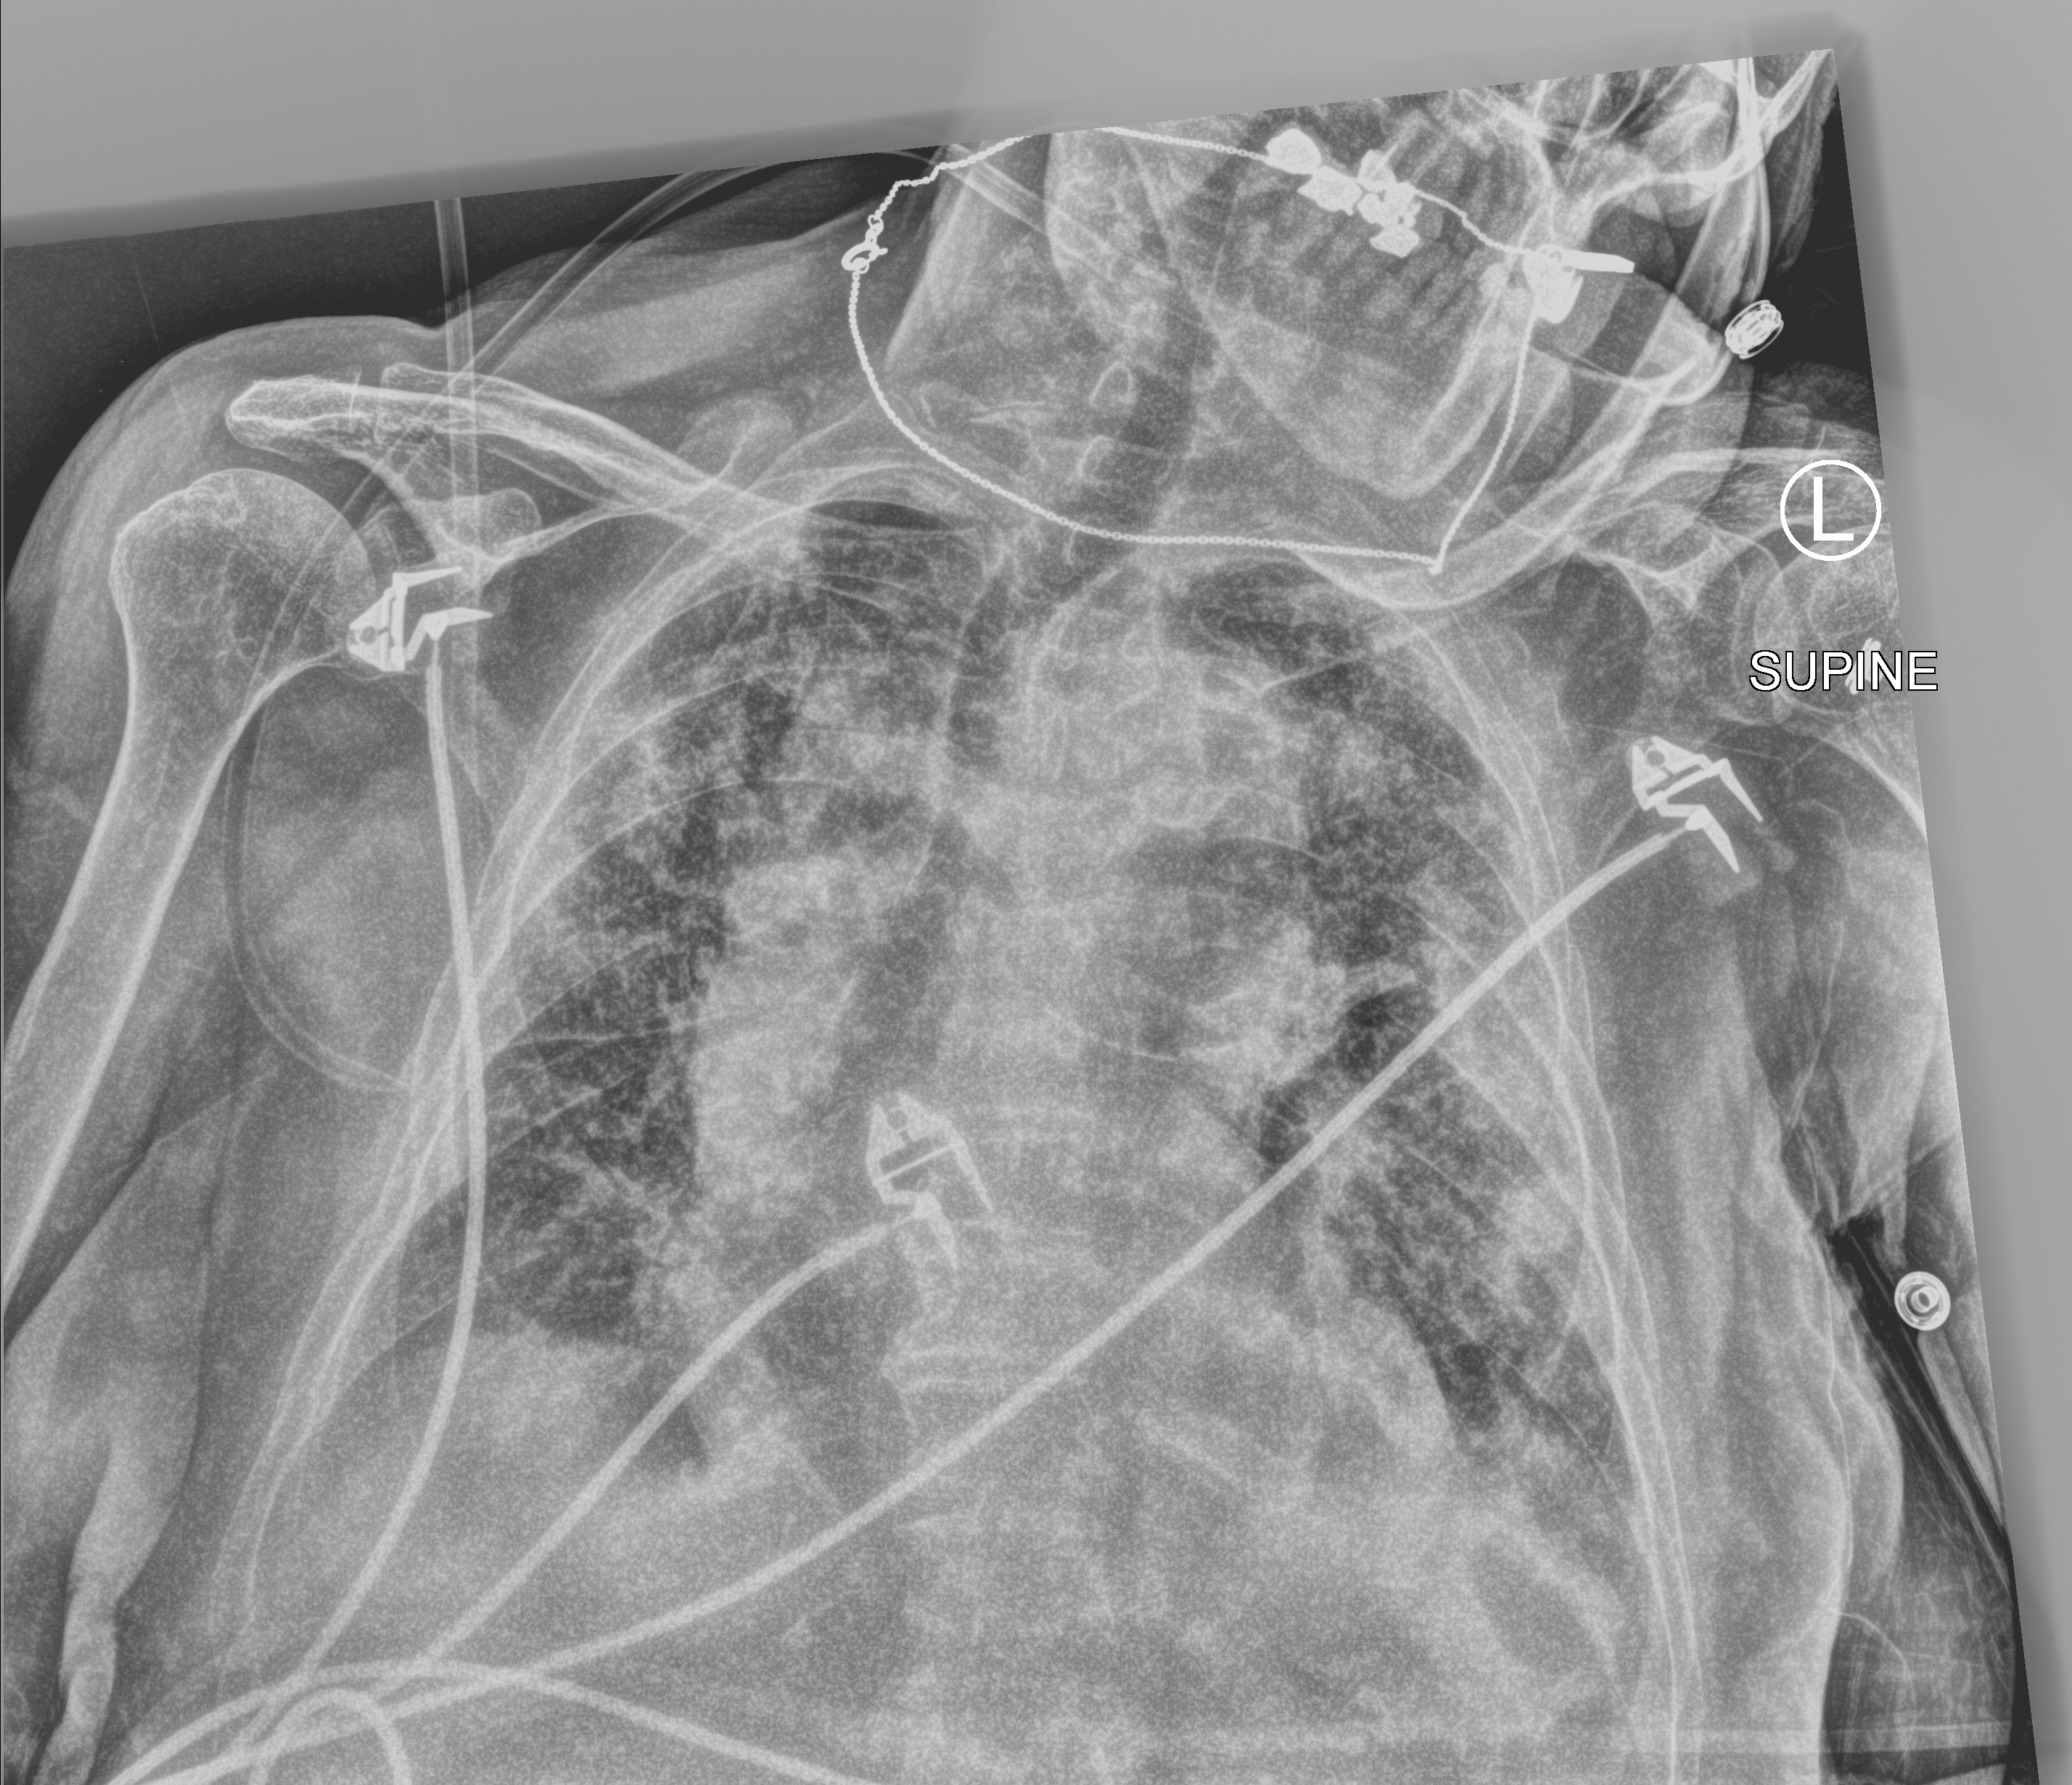
Chest X-ray (portable); anteroposterior (AP) projection. Female patient hospitalised with COVID-19, age 75–90 years.
Hospital-stay facts (about this admission, not read from this image; timing relative to this image not recorded):
- length of hospital stay: 13 days